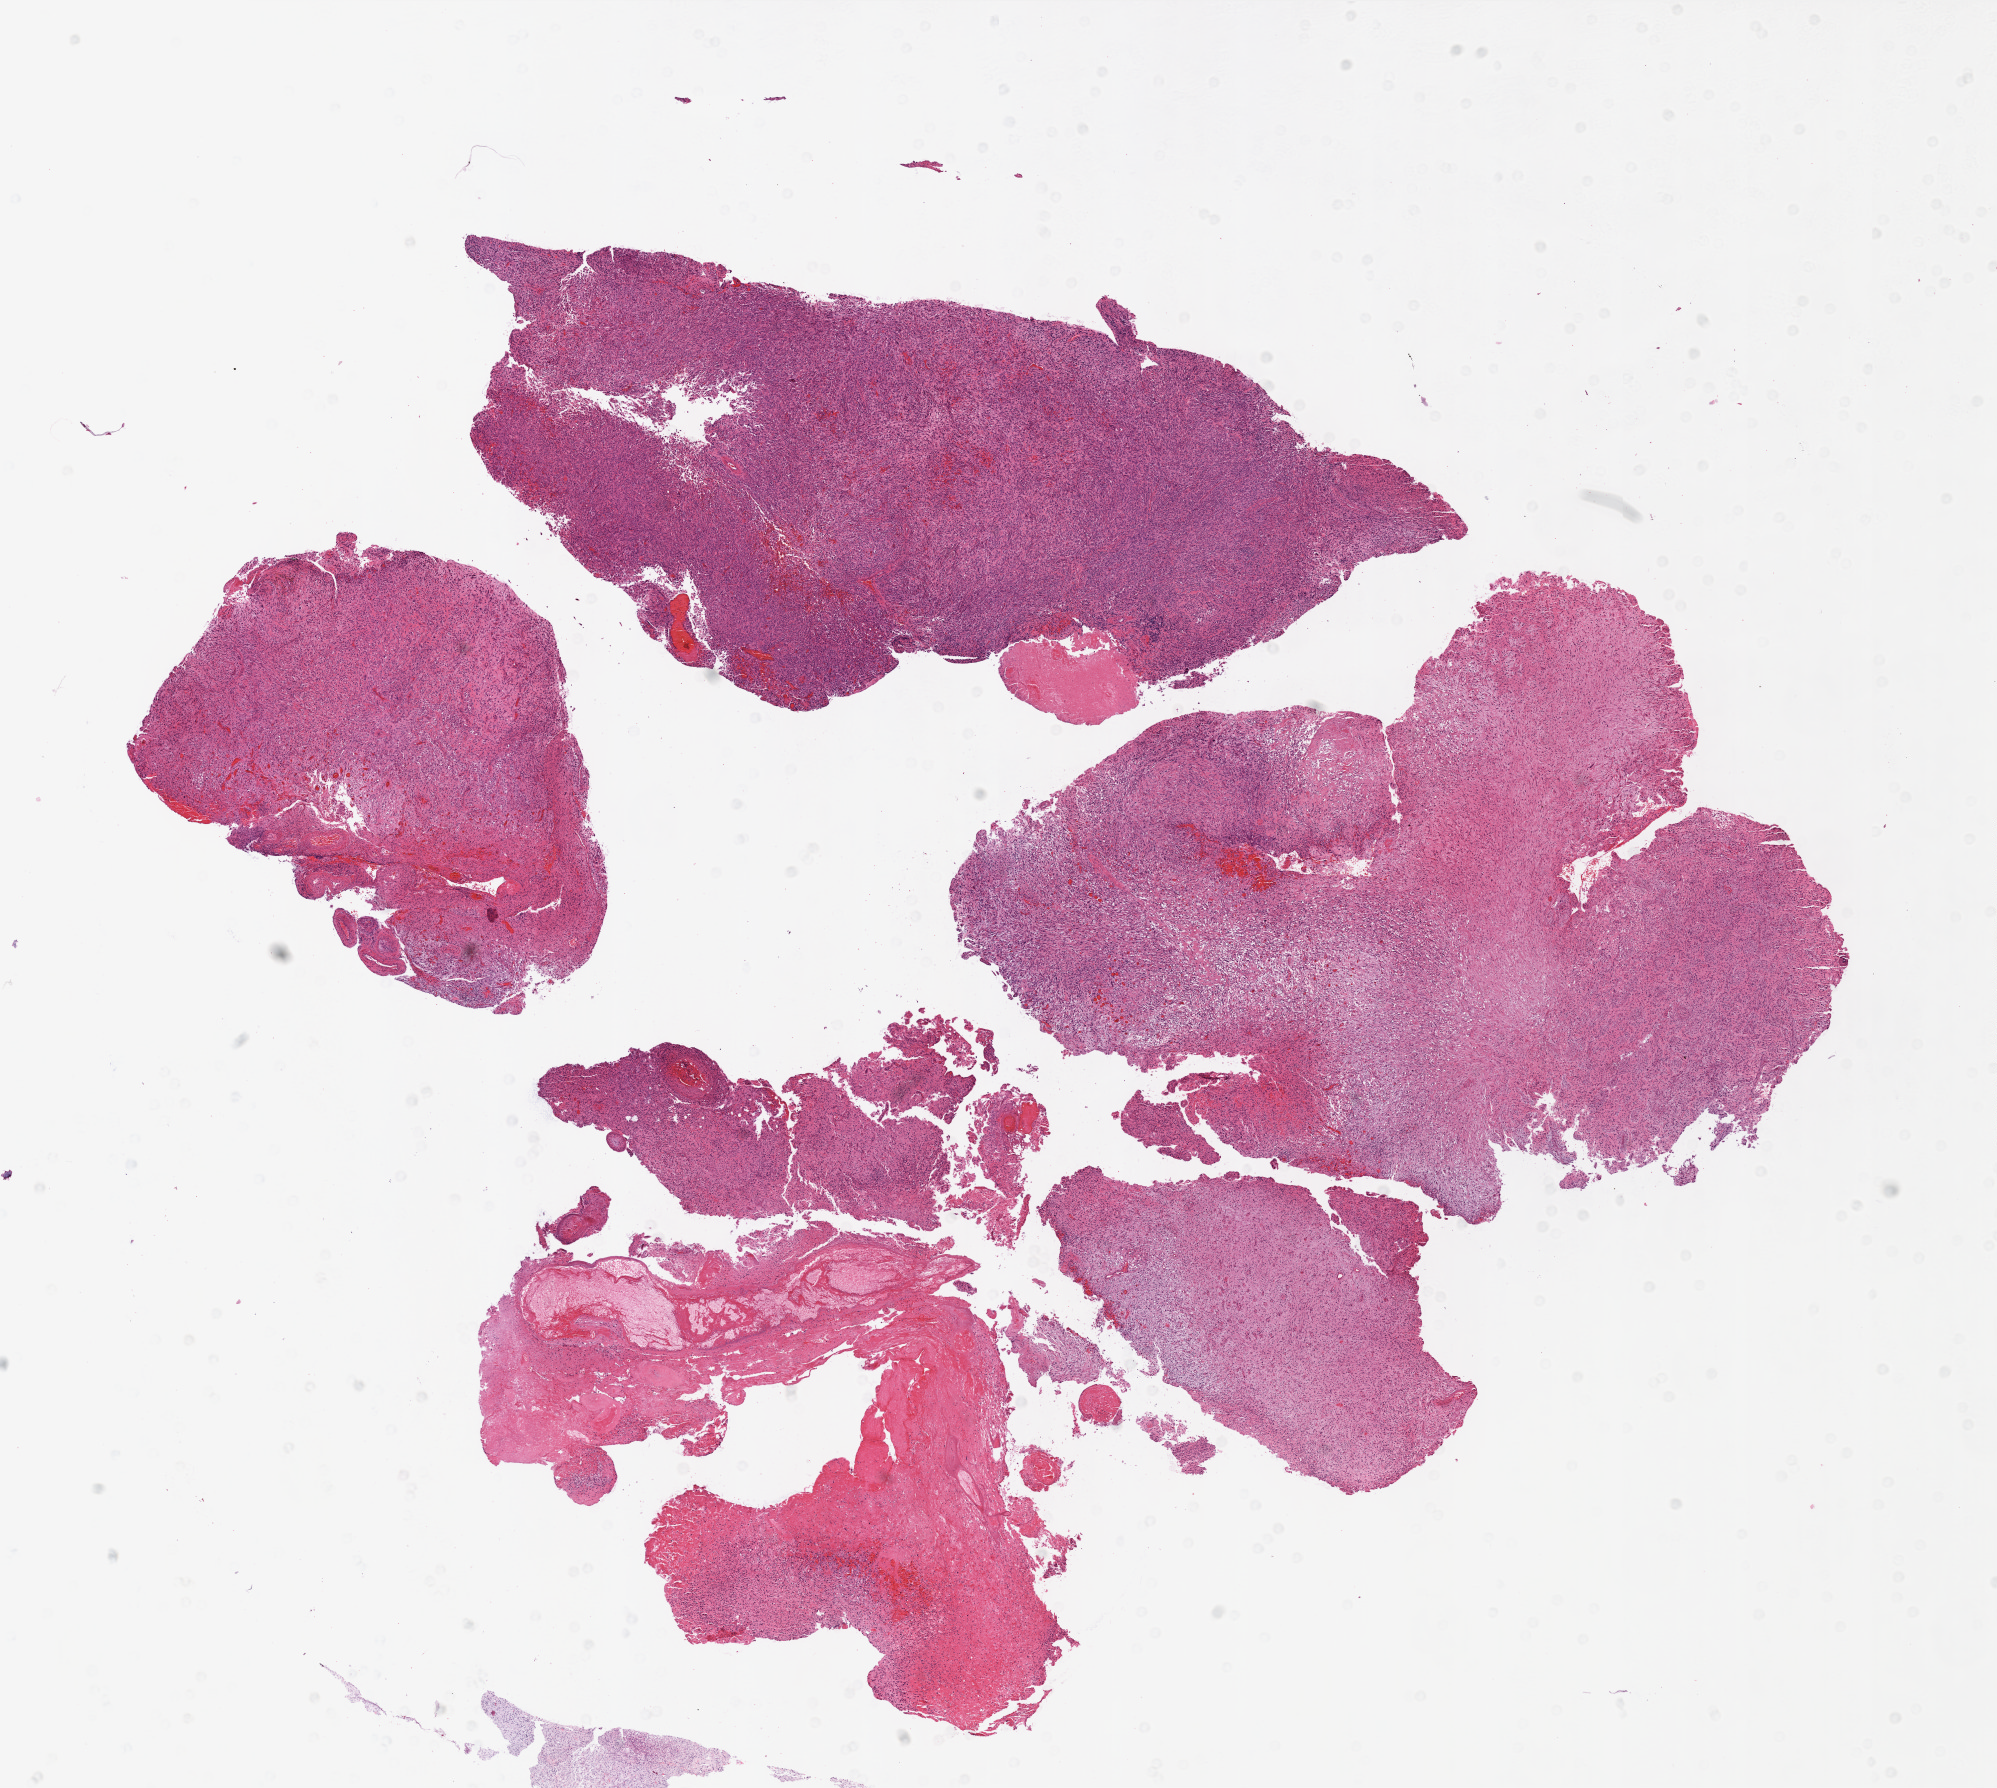
Whole-slide histology image, Hematoxylin and eosin (H&E) stained — shown as a low-resolution overview of the whole scanned area (about 16.0 x 14.3 mm, from a 20x scan), FFPE section, sample: primary tumour, brain. Male patient; age at initial diagnosis 40 years.
Diagnosis: Glioblastoma.